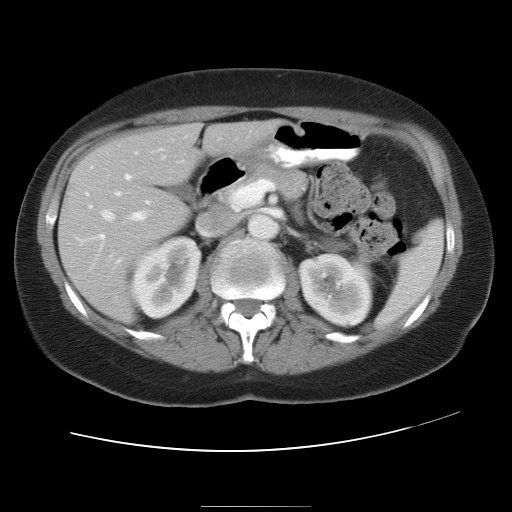
Contrast-enhanced abdominal CT, one axial slice; position 17 of 30 along the scan axis; reconstruction kernel STANDARD; 120 kVp; soft-tissue window (W 400 / L 40 HU); 7.5 mm slice thickness; 512 × 512 image matrix. Female patient, age 52 years. From the clinical record (not read from this slice): diagnosis: colorectal cancer liver metastases, imaged before liver resection; multiple liver metastases: no; largest metastasis: 3 cm; chemotherapy before resection: yes.
Annotated regions visible in this slice (outlined manually by an expert reader):
- hepatic veins: bounding box (x1, y1, x2, y2) in pixels: (102, 156, 164, 221)
- liver: (59, 121, 277, 322)
- planned liver remnant (the part of the liver to remain after resection): (159, 121, 276, 171)
- portal vein (with intrahepatic branches): (99, 175, 149, 239)